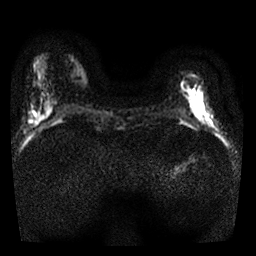
Breast MRI, one axial slice; diffusion-weighted series; image 2 of 4 stored at this slice position (different b-values; order by instance number); 1.5 T; 256 × 256 image matrix, field of view 300 × 300 mm. Female patient.
Outlined on this slice (expert manual segmentation):
- tumour on diffusion-weighted imaging: box from (x=186, y=89) to (x=213, y=128) px